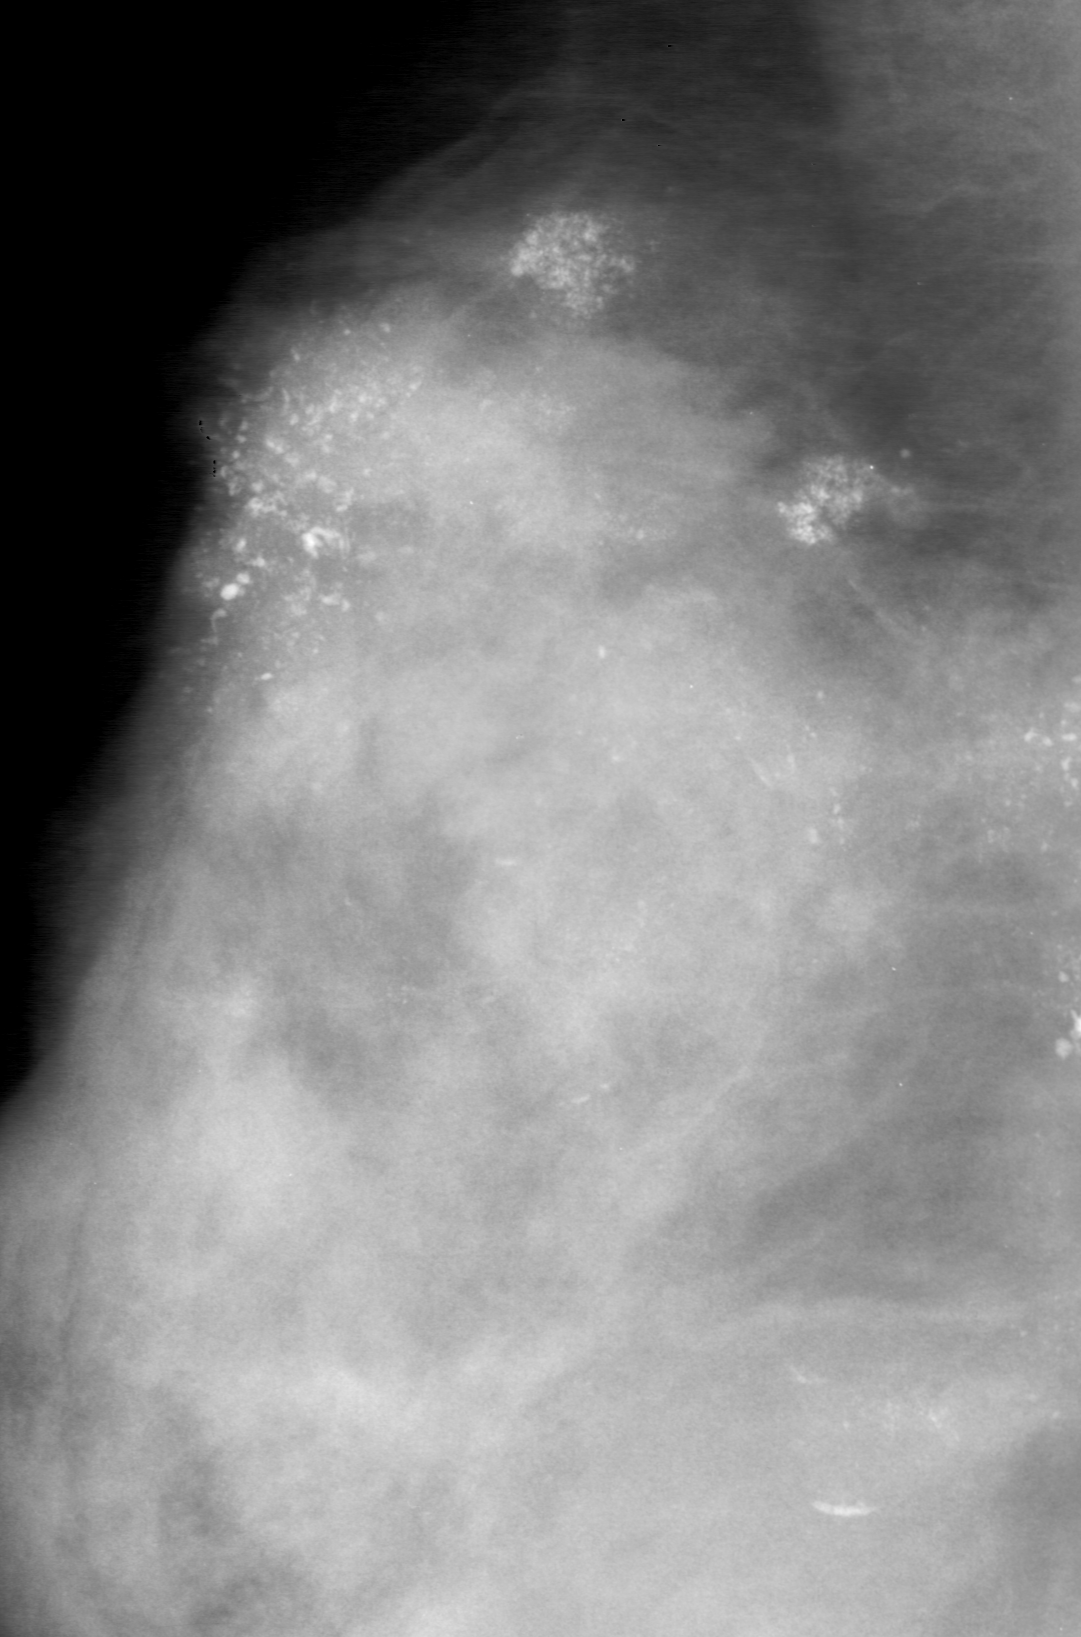
Cropped region of a digitized screen-film mammogram centred on a radiologist-marked abnormality; right breast; MLO view; BI-RADS breast density category 4 (scale 1–4).
Calcifications, morphology pleomorphic, distribution segmental; BI-RADS assessment category 5; subtlety rating 5 on a 1 (subtle) to 5 (obvious) scale; pathology result (as recorded, not read from the image): malignant.